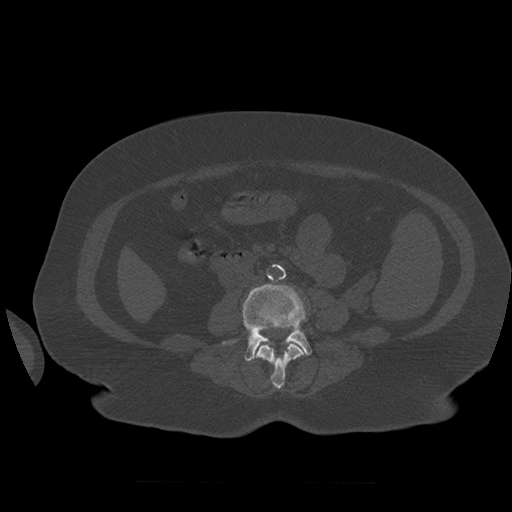
CT including the spine, one axial slice; position 216 of 399 along the scan axis; reconstruction kernel STANDARD; bone window (W 1800 / L 400 HU); 1.25 mm slice thickness; 512 × 512 image matrix, field of view 404 × 404 mm. Patient age 81 years. Case-level facts recorded for this patient, not image findings: primary cancer: renal; vertebrae with lytic lesions (as recorded): L1.
Outlined on this slice (semi-automatically segmented with operator editing):
- L3 vertebra: bounding box [x1, y1, x2, y2] px = [255, 342, 305, 389]
- L4 vertebra: [223, 284, 312, 362]